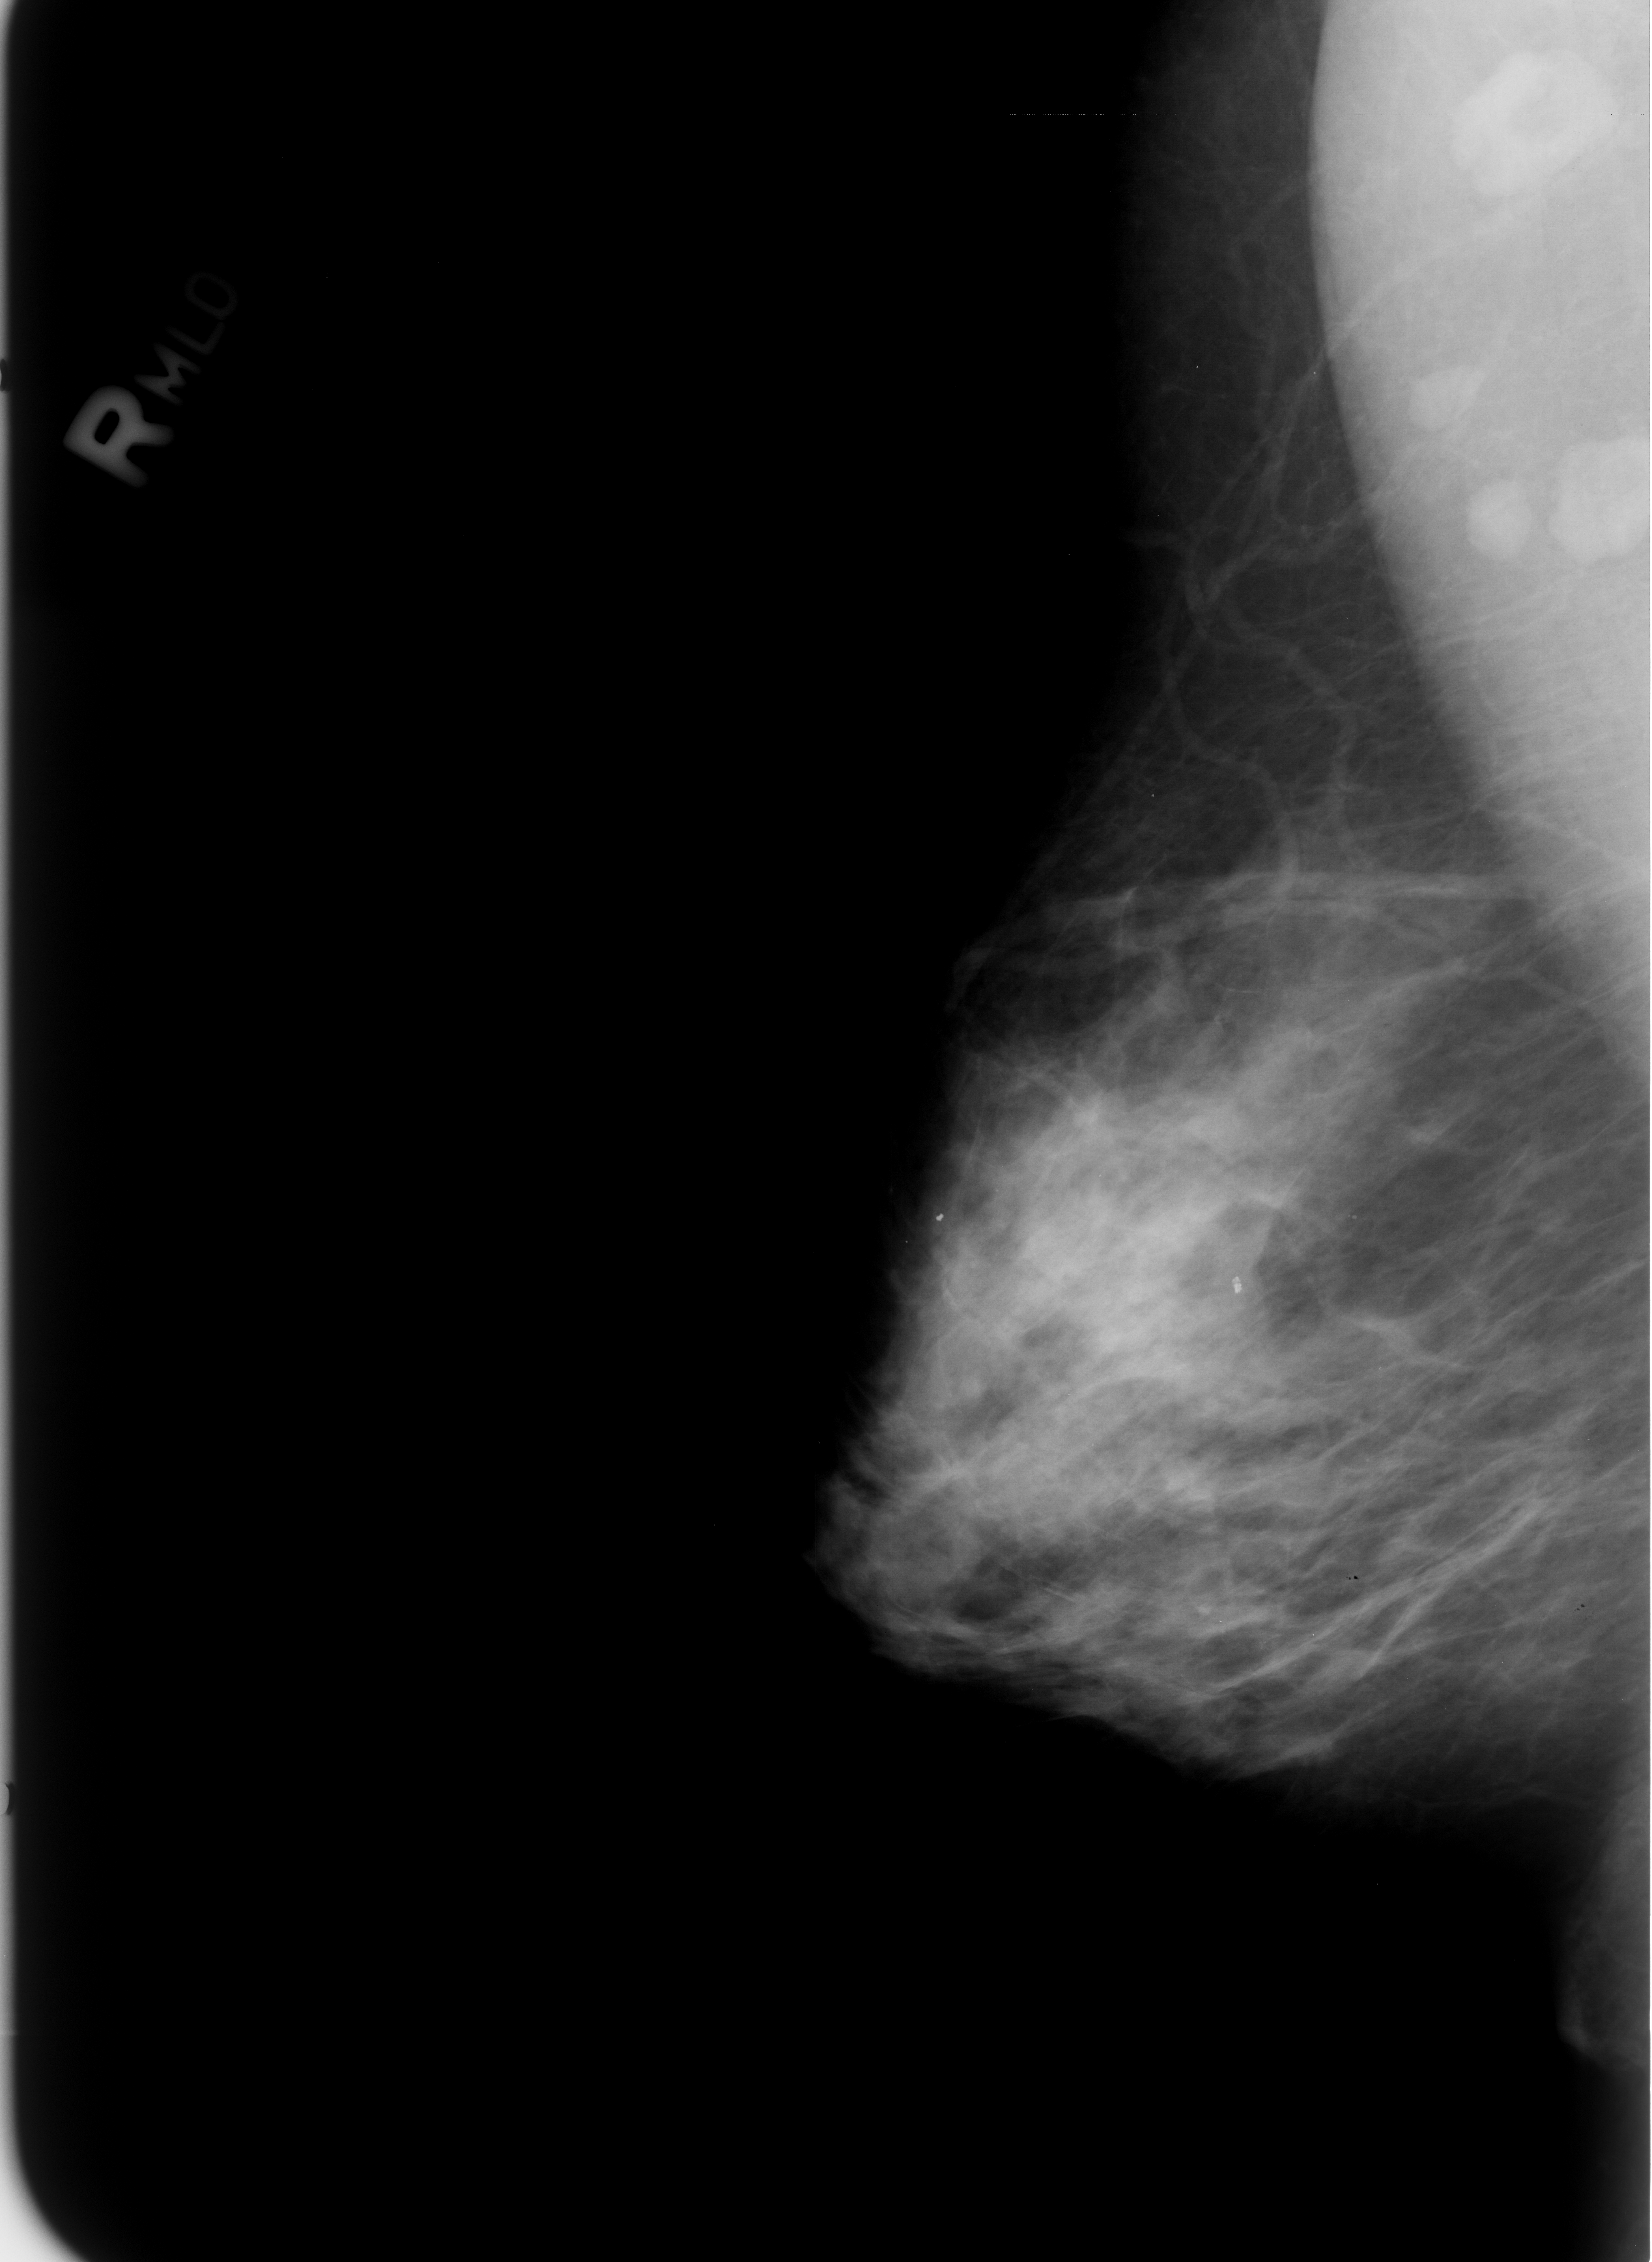
Mammogram (digitized film); right breast; MLO view; breast composition: heterogeneously dense (BI-RADS density category 3 of 4).
Abnormality record for this image: Finding 1 of 2: calcifications, morphology lucent center; BI-RADS assessment category 2; benign without callback (not worked up further). Finding 2 of 2: calcifications, morphology lucent center; BI-RADS assessment category 2; benign; no additional work-up was recommended (benign without callback).